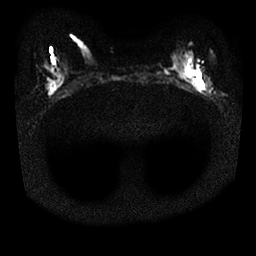
Breast MRI, one axial slice. Slice 10 of 25 in the series (ordered by position). Diffusion-weighted series; image 2 of 4 stored at this slice position (different b-values; order by instance number). 1.5 T. 4 mm slice thickness. 256 × 256 image matrix. Female patient.
Annotated regions visible in this slice (outlined manually by an expert reader):
- tumour on diffusion-weighted imaging: bounding box [x1, y1, x2, y2] px = [186, 69, 201, 88]